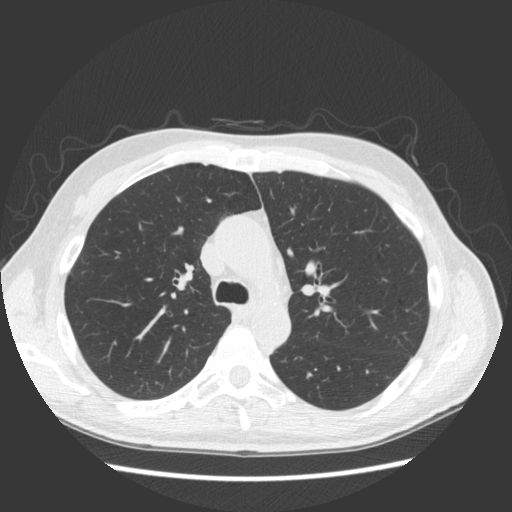
Axial slice from a low-dose chest CT screening exam; second annual screen; lung window (W 1500 / L -600 HU); 2.5 mm slice thickness; slice 58 of 163 in the series; 512 × 512 image matrix, field of view 360 × 360 mm. Male, age 57 years at enrolment. Former smoker at enrolment.
• Lesion marked by an expert reader, bounding box <153,253,203,299> (left, top, right, bottom; pixels).
• The screening reader recorded 3 non-calcified nodules or masses ≥4 mm on this exam (right middle lobe, right middle lobe, right middle lobe); which of them this box marks is not recorded.
• Lung cancer was diagnosed 264 days after this screen: adenocarcinoma, NOS, right upper lobe, poorly differentiated (G3), stage IB (AJCC 6th edition), 25 mm at pathology.